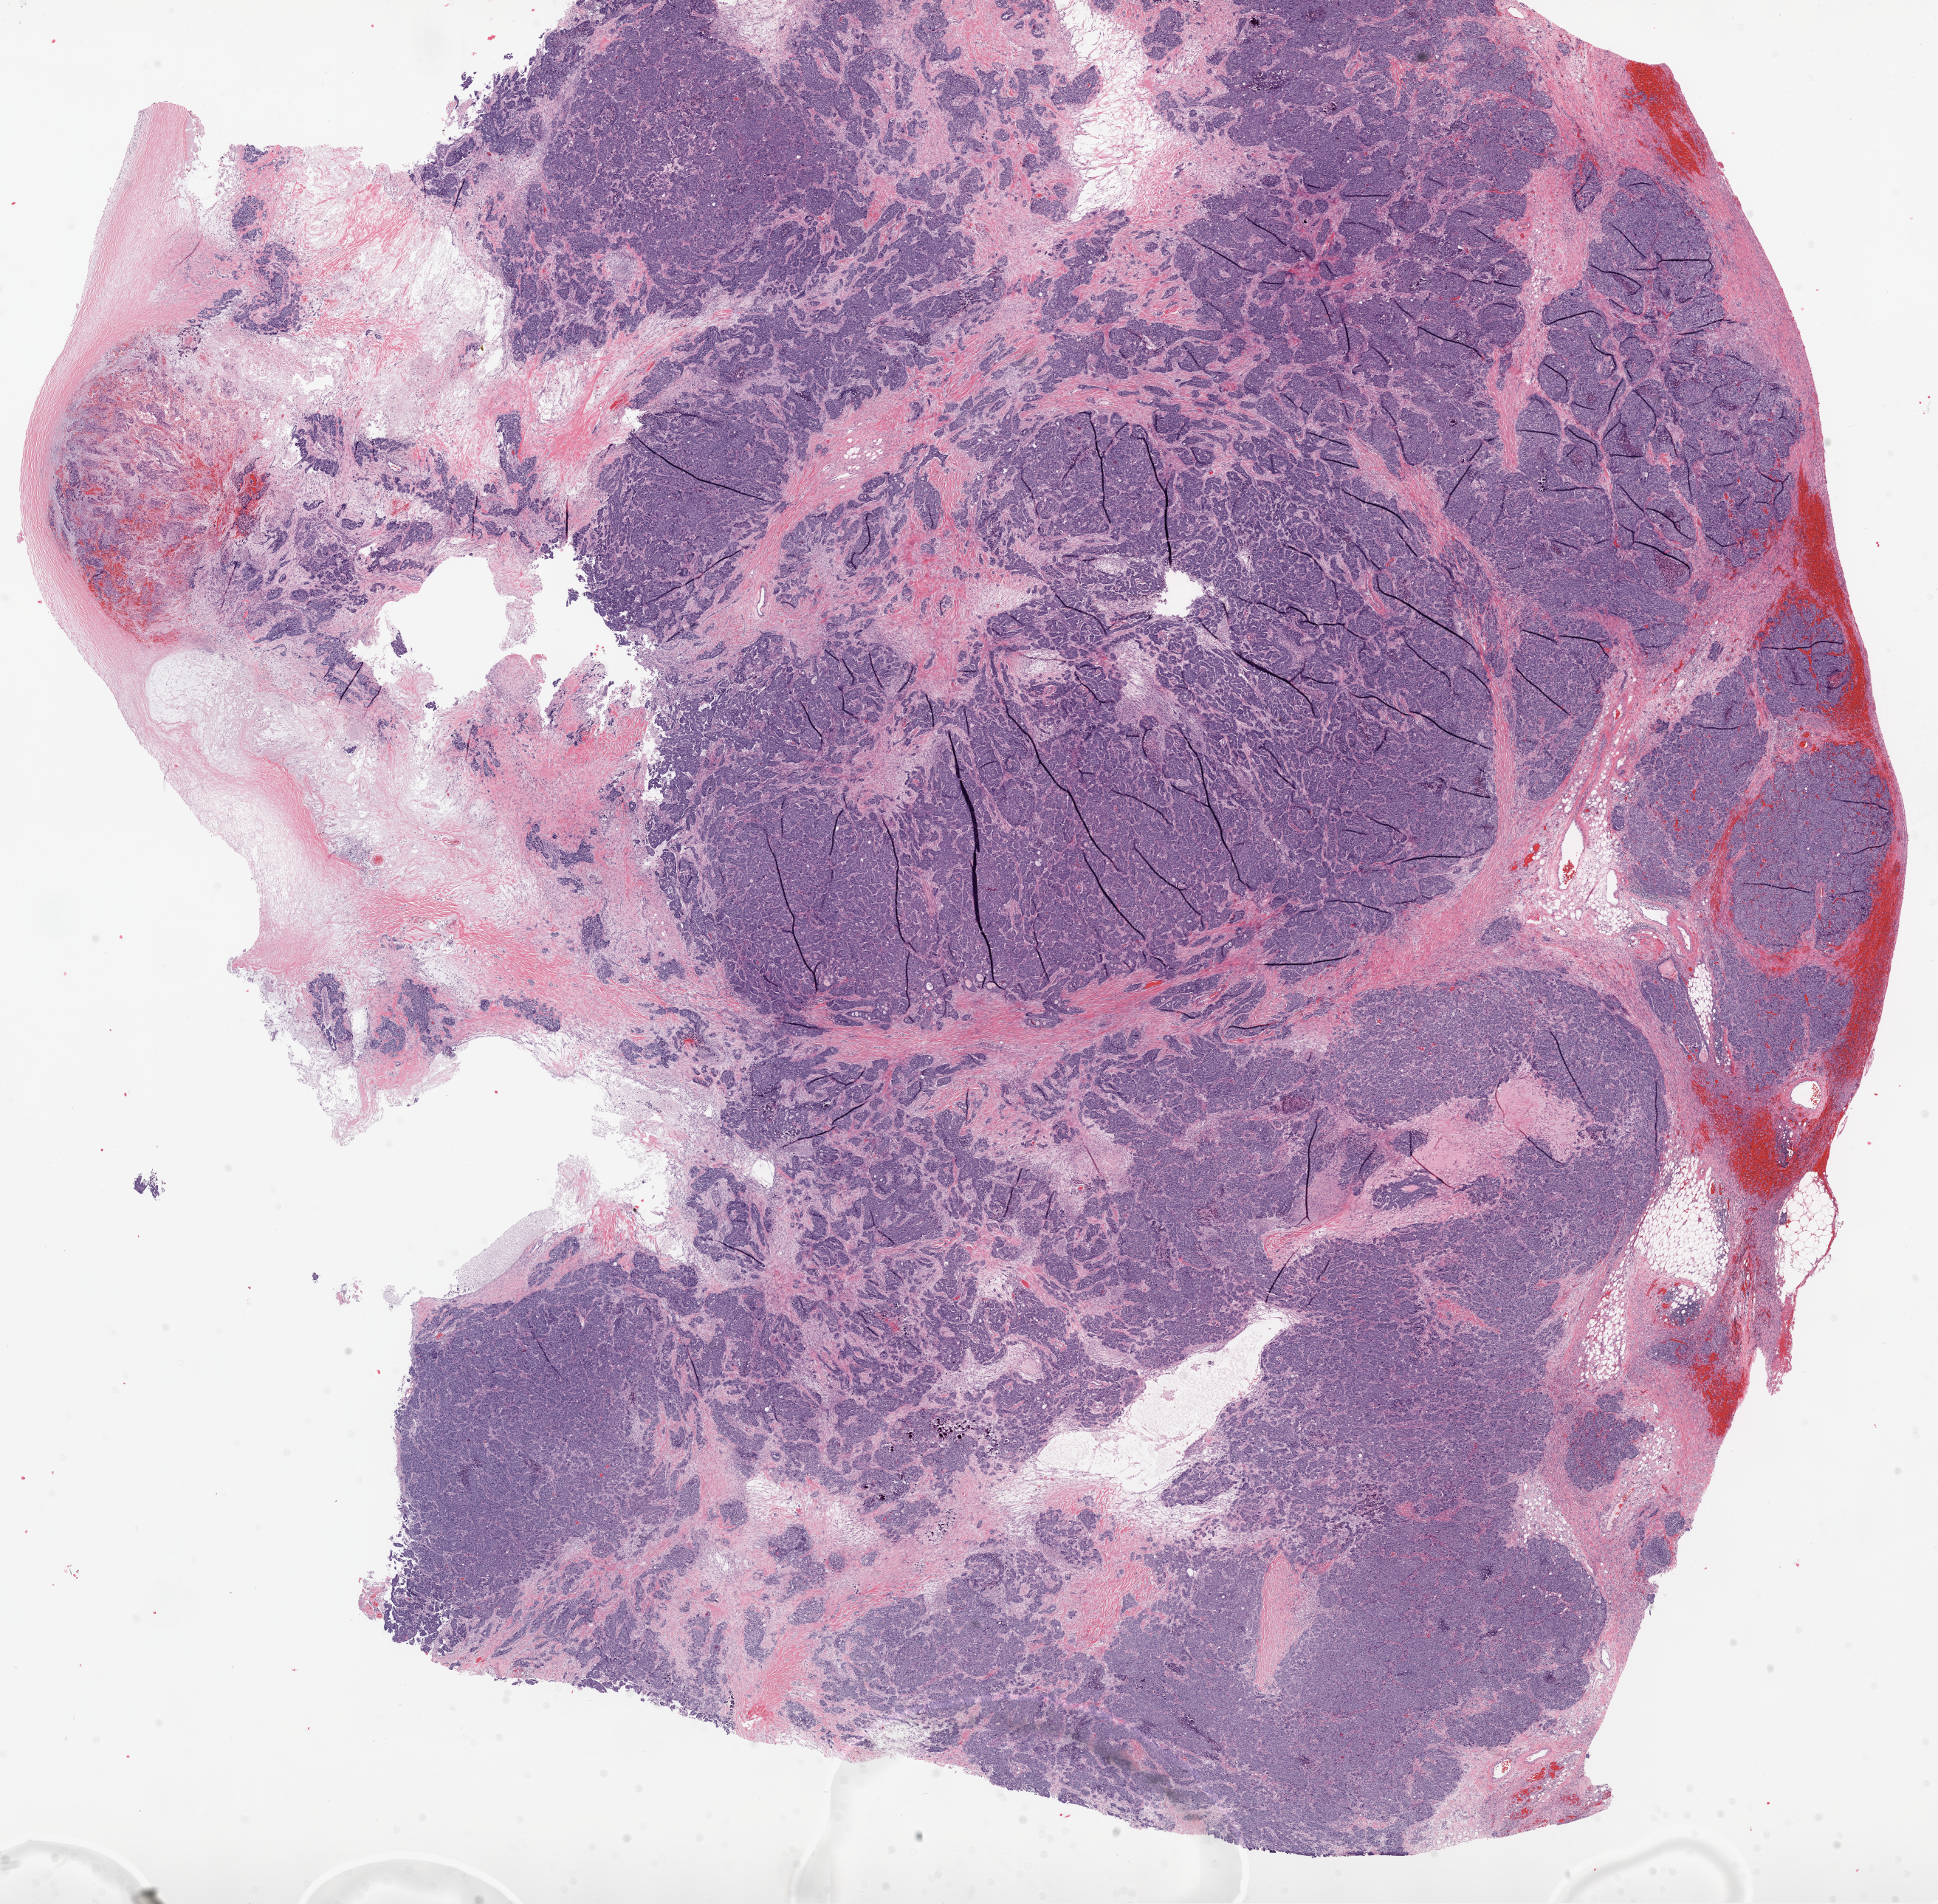
Digitized H&E-stained tissue section (whole slide), shown as a low-resolution overview of the whole scanned area (about 21.1 x 20.7 mm); frozen section from the top of the tissue portion; sample: primary tumour, ovary. Female patient; age at initial diagnosis 57 years. Histologic grade: G3 (poorly differentiated). Pathologist review of this section (percent, as recorded): tumour cells 77%, tumour nuclei 85%, normal cells 0%, stromal cells 15%, necrosis 8%.
Histologic diagnosis: Serous cystadenocarcinoma, NOS. FIGO stage: IIIC.